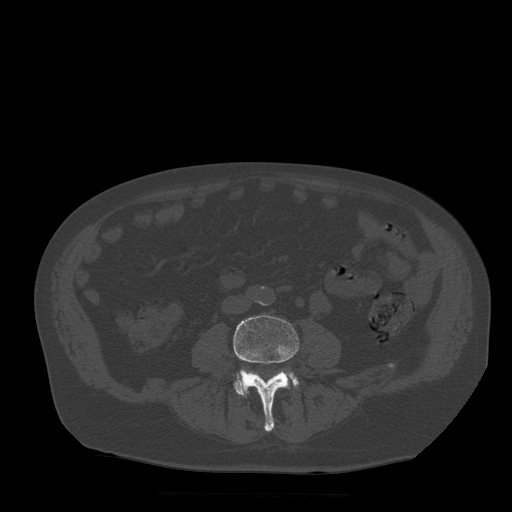
CT including the spine, one axial slice; slice 112 of 522 in the series (ordered by position); bone window (W 1800 / L 400 HU); 1.25 mm slice thickness; 512 × 512 image matrix, field of view 420 × 420 mm. Patient age 72 years. Case-level facts recorded for this patient, not image findings: primary cancer: prostate.
Structures marked on this image (semi-automatic segmentation, software-assisted and operator-edited):
- L4 vertebra: bounding box (x1, y1, x2, y2) in pixels: (233, 315, 299, 432)
- L5 vertebra: (235, 371, 299, 396)